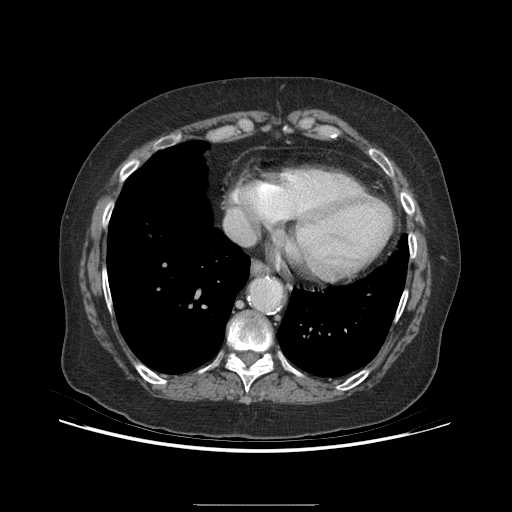
Contrast-enhanced abdominal CT (liver protocol), one axial slice; position 187 of 192 along the scan axis; 140 kVp; soft-tissue window (W 400 / L 40 HU); 2.5 mm slice thickness; 512 × 512 image matrix. Case-level facts recorded for this patient, not image findings: diagnosis: hepatocellular carcinoma (patient treated with transarterial chemoembolisation; whether this scan precedes or follows treatment is not stated here); TNM stage (as recorded): Stage-I; Child-Pugh class: A; tumour differentiation: moderately differentiated; tumour nodularity: uninodular.
Annotated regions visible in this slice (semi-automatically segmented with operator editing):
- abdominal aorta: bounding box [x1, y1, x2, y2] px = [251, 280, 280, 309]